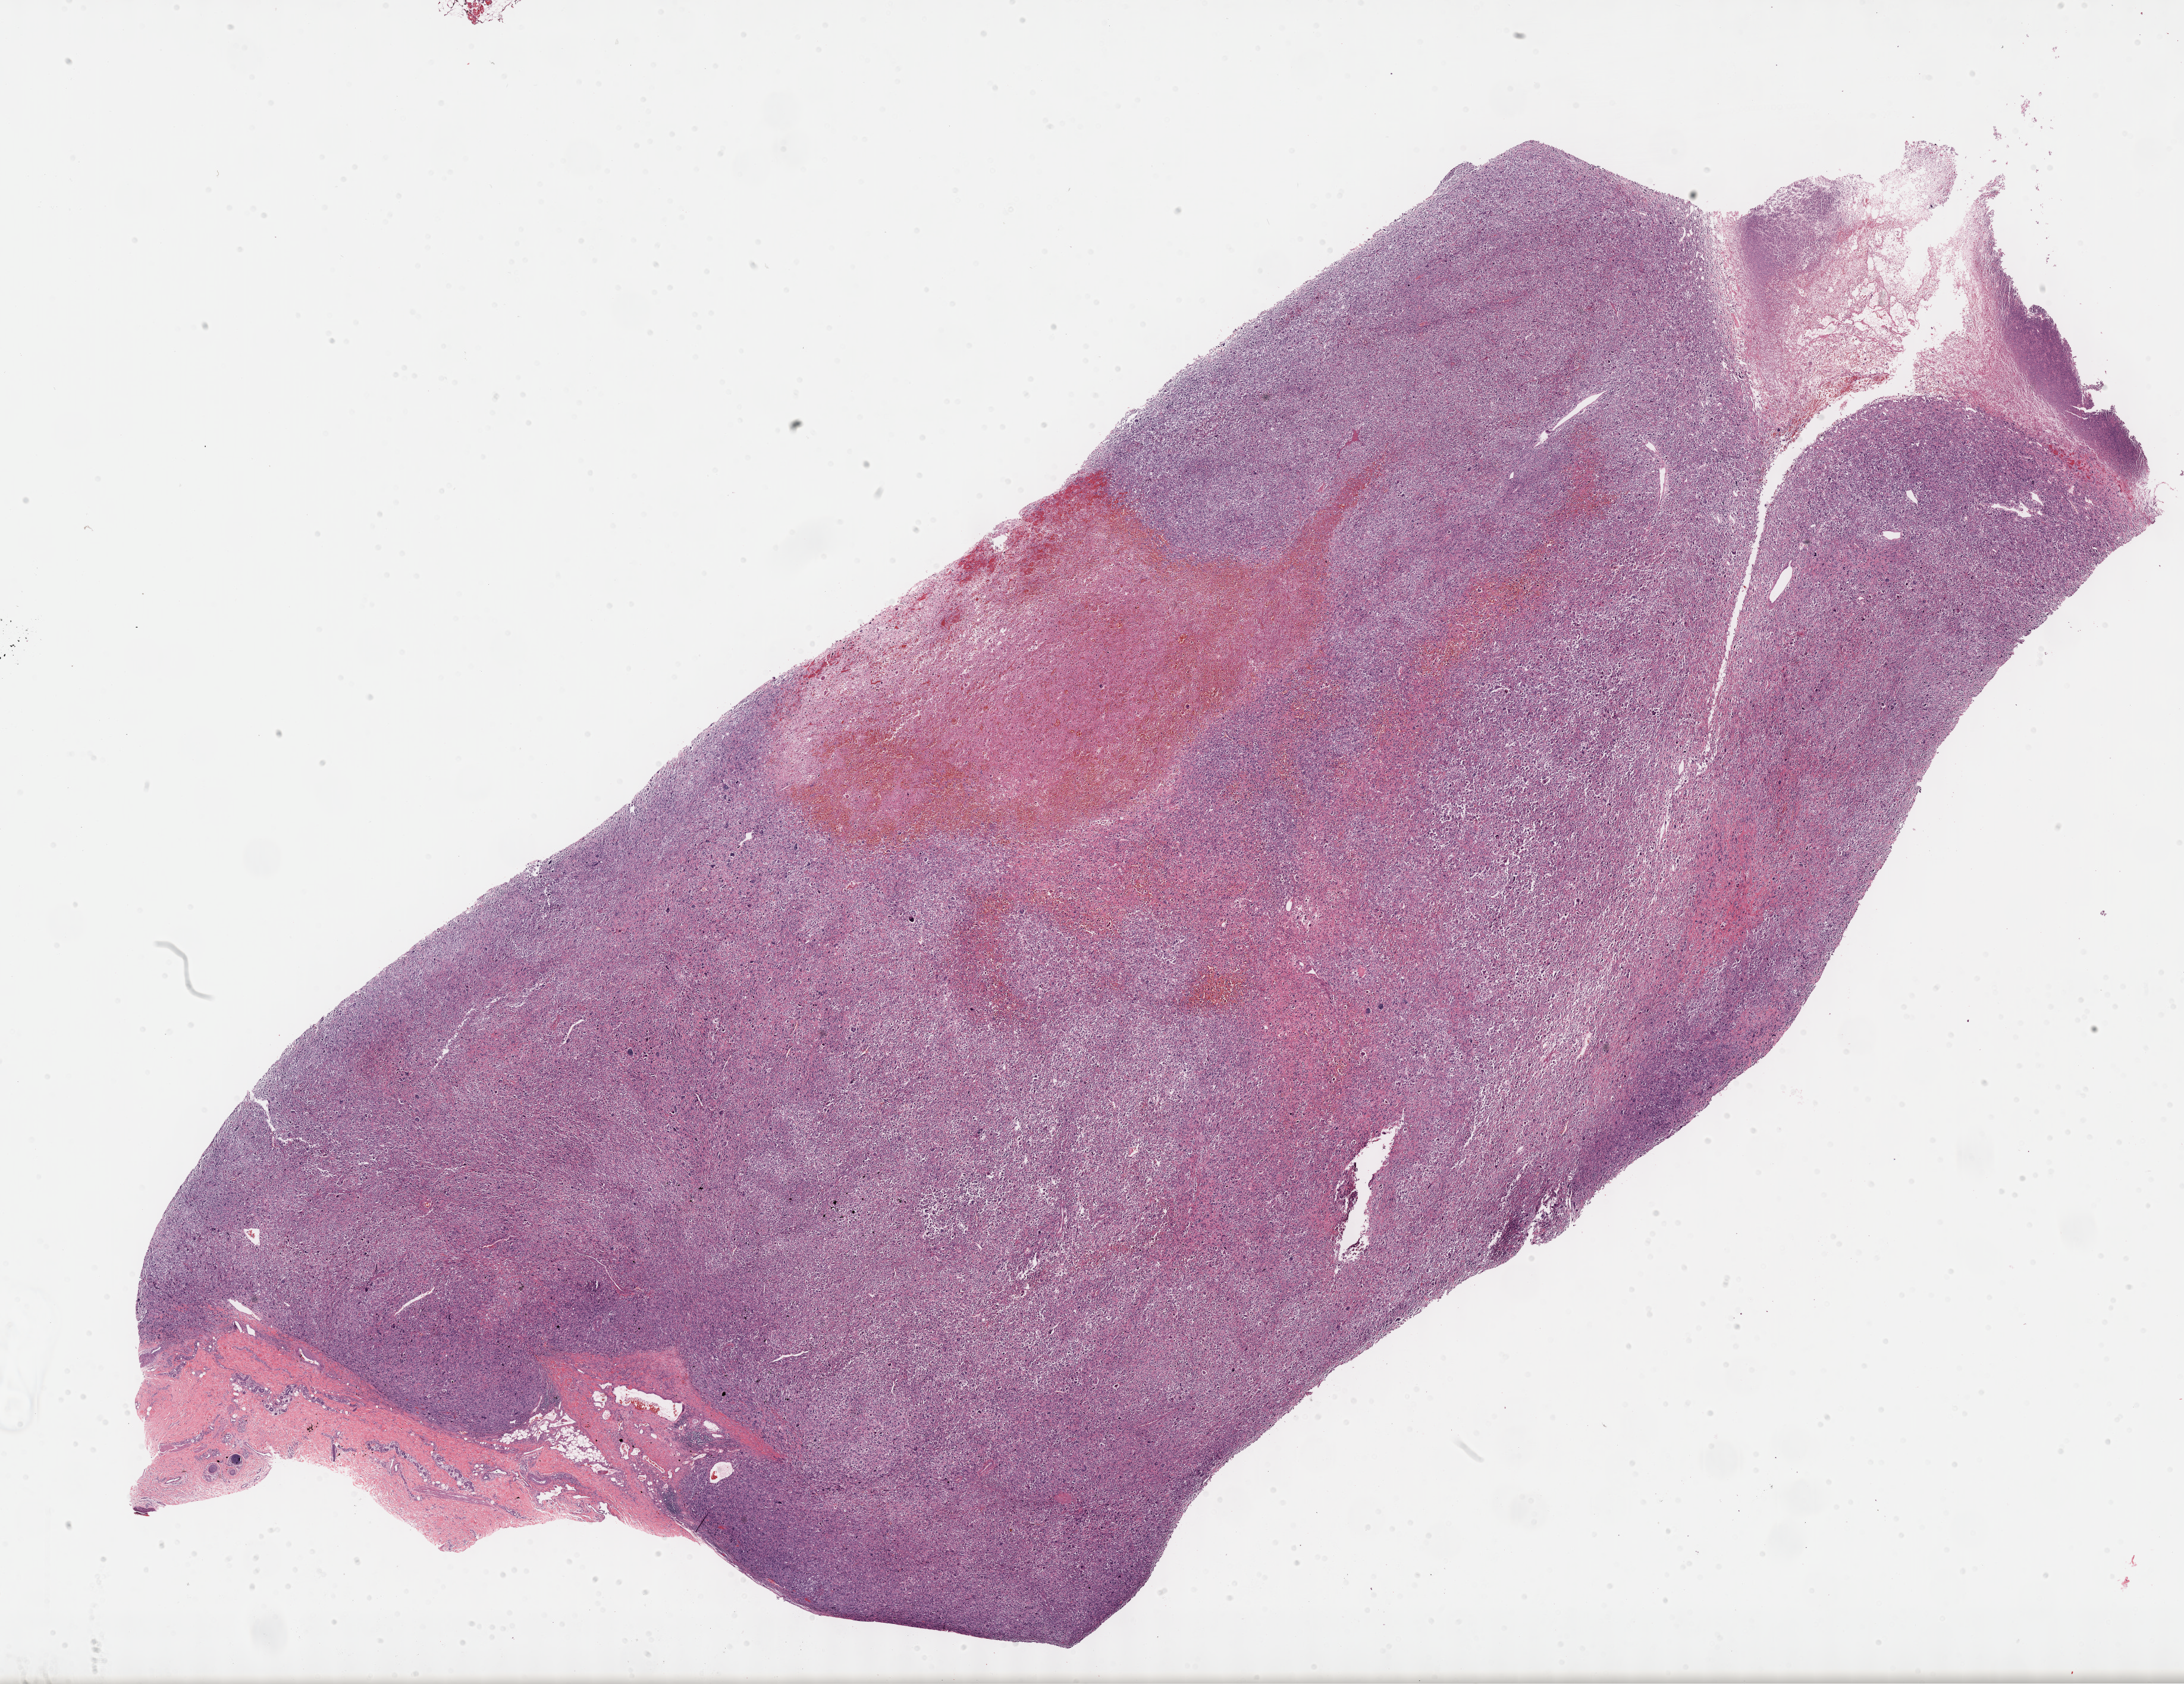
H&E-stained whole-slide image, a low-resolution overview of the entire scanned area, about 29.7 x 22.9 mm (slide scanned at 40x). Formalin-fixed paraffin-embedded (FFPE) diagnostic section. Connective, subcutaneous and other soft tissues, primary tumour sample. Female, age 78 years at initial diagnosis.
Diagnosis: Malignant fibrous histiocytoma (connective, subcutaneous and other soft tissues of lower limb and hip).